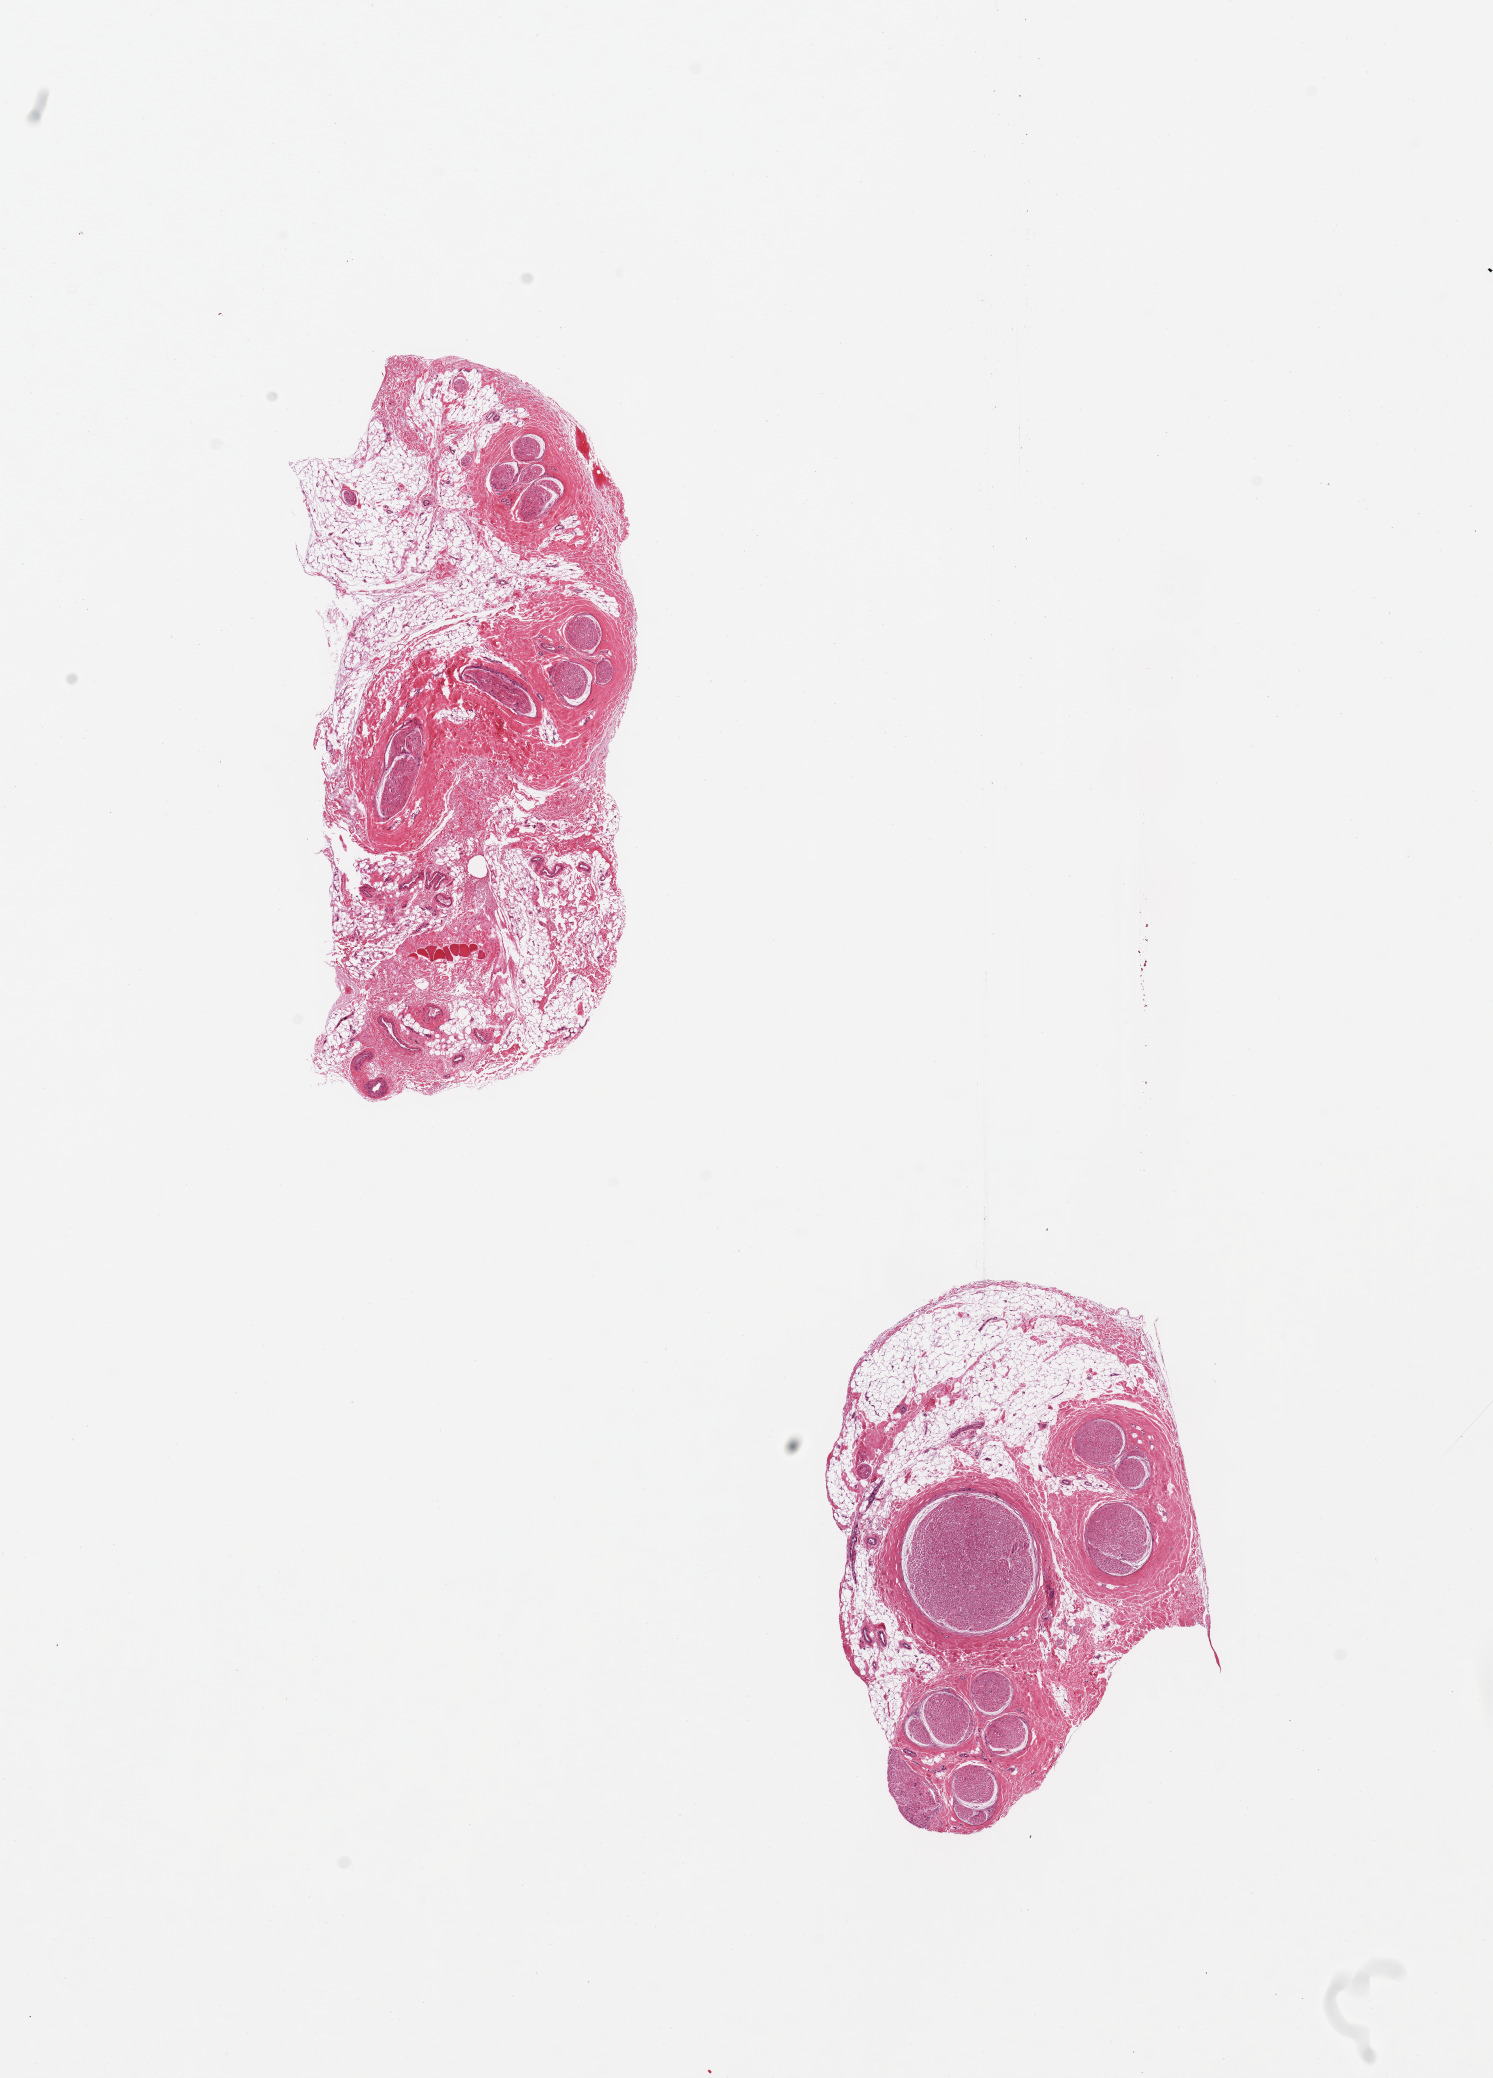
H&E whole-slide image — whole scanned area (about 11.8 x 16.4 mm, slide scanned at 20x) shown as a low-resolution overview; PAXgene-fixed paraffin-embedded (PFPE) section; section of tibial nerve (target tissue); tissue donor sample. Donor: male.
Review note (as recorded): 2 pieces, ~60-70% adherent fat/fibrous tissue, only ~30% target peripheral nerve.